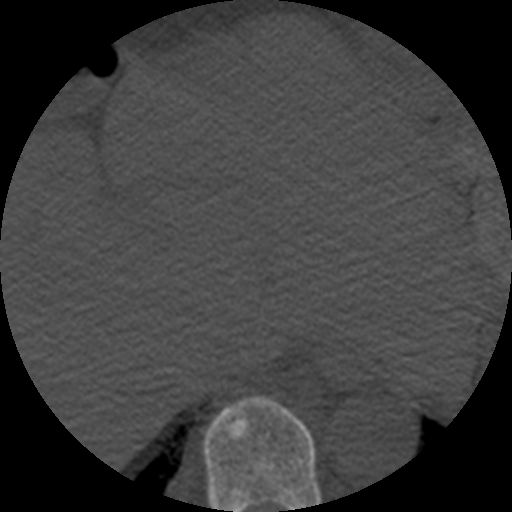
CT including the spine, one axial slice. Position 287 of 508 along the scan axis. Reconstruction kernel STANDARD. 120 kVp. Bone window (W 1800 / L 400 HU). 512 × 512 image matrix, field of view 160 × 160 mm. Patient age 57 years. From the clinical record (not read from this slice): primary cancer: prostate.
Outlined on this slice (semi-automatically segmented with operator editing):
- T9 vertebra: bounding box [x1, y1, x2, y2] px = [203, 396, 322, 512]